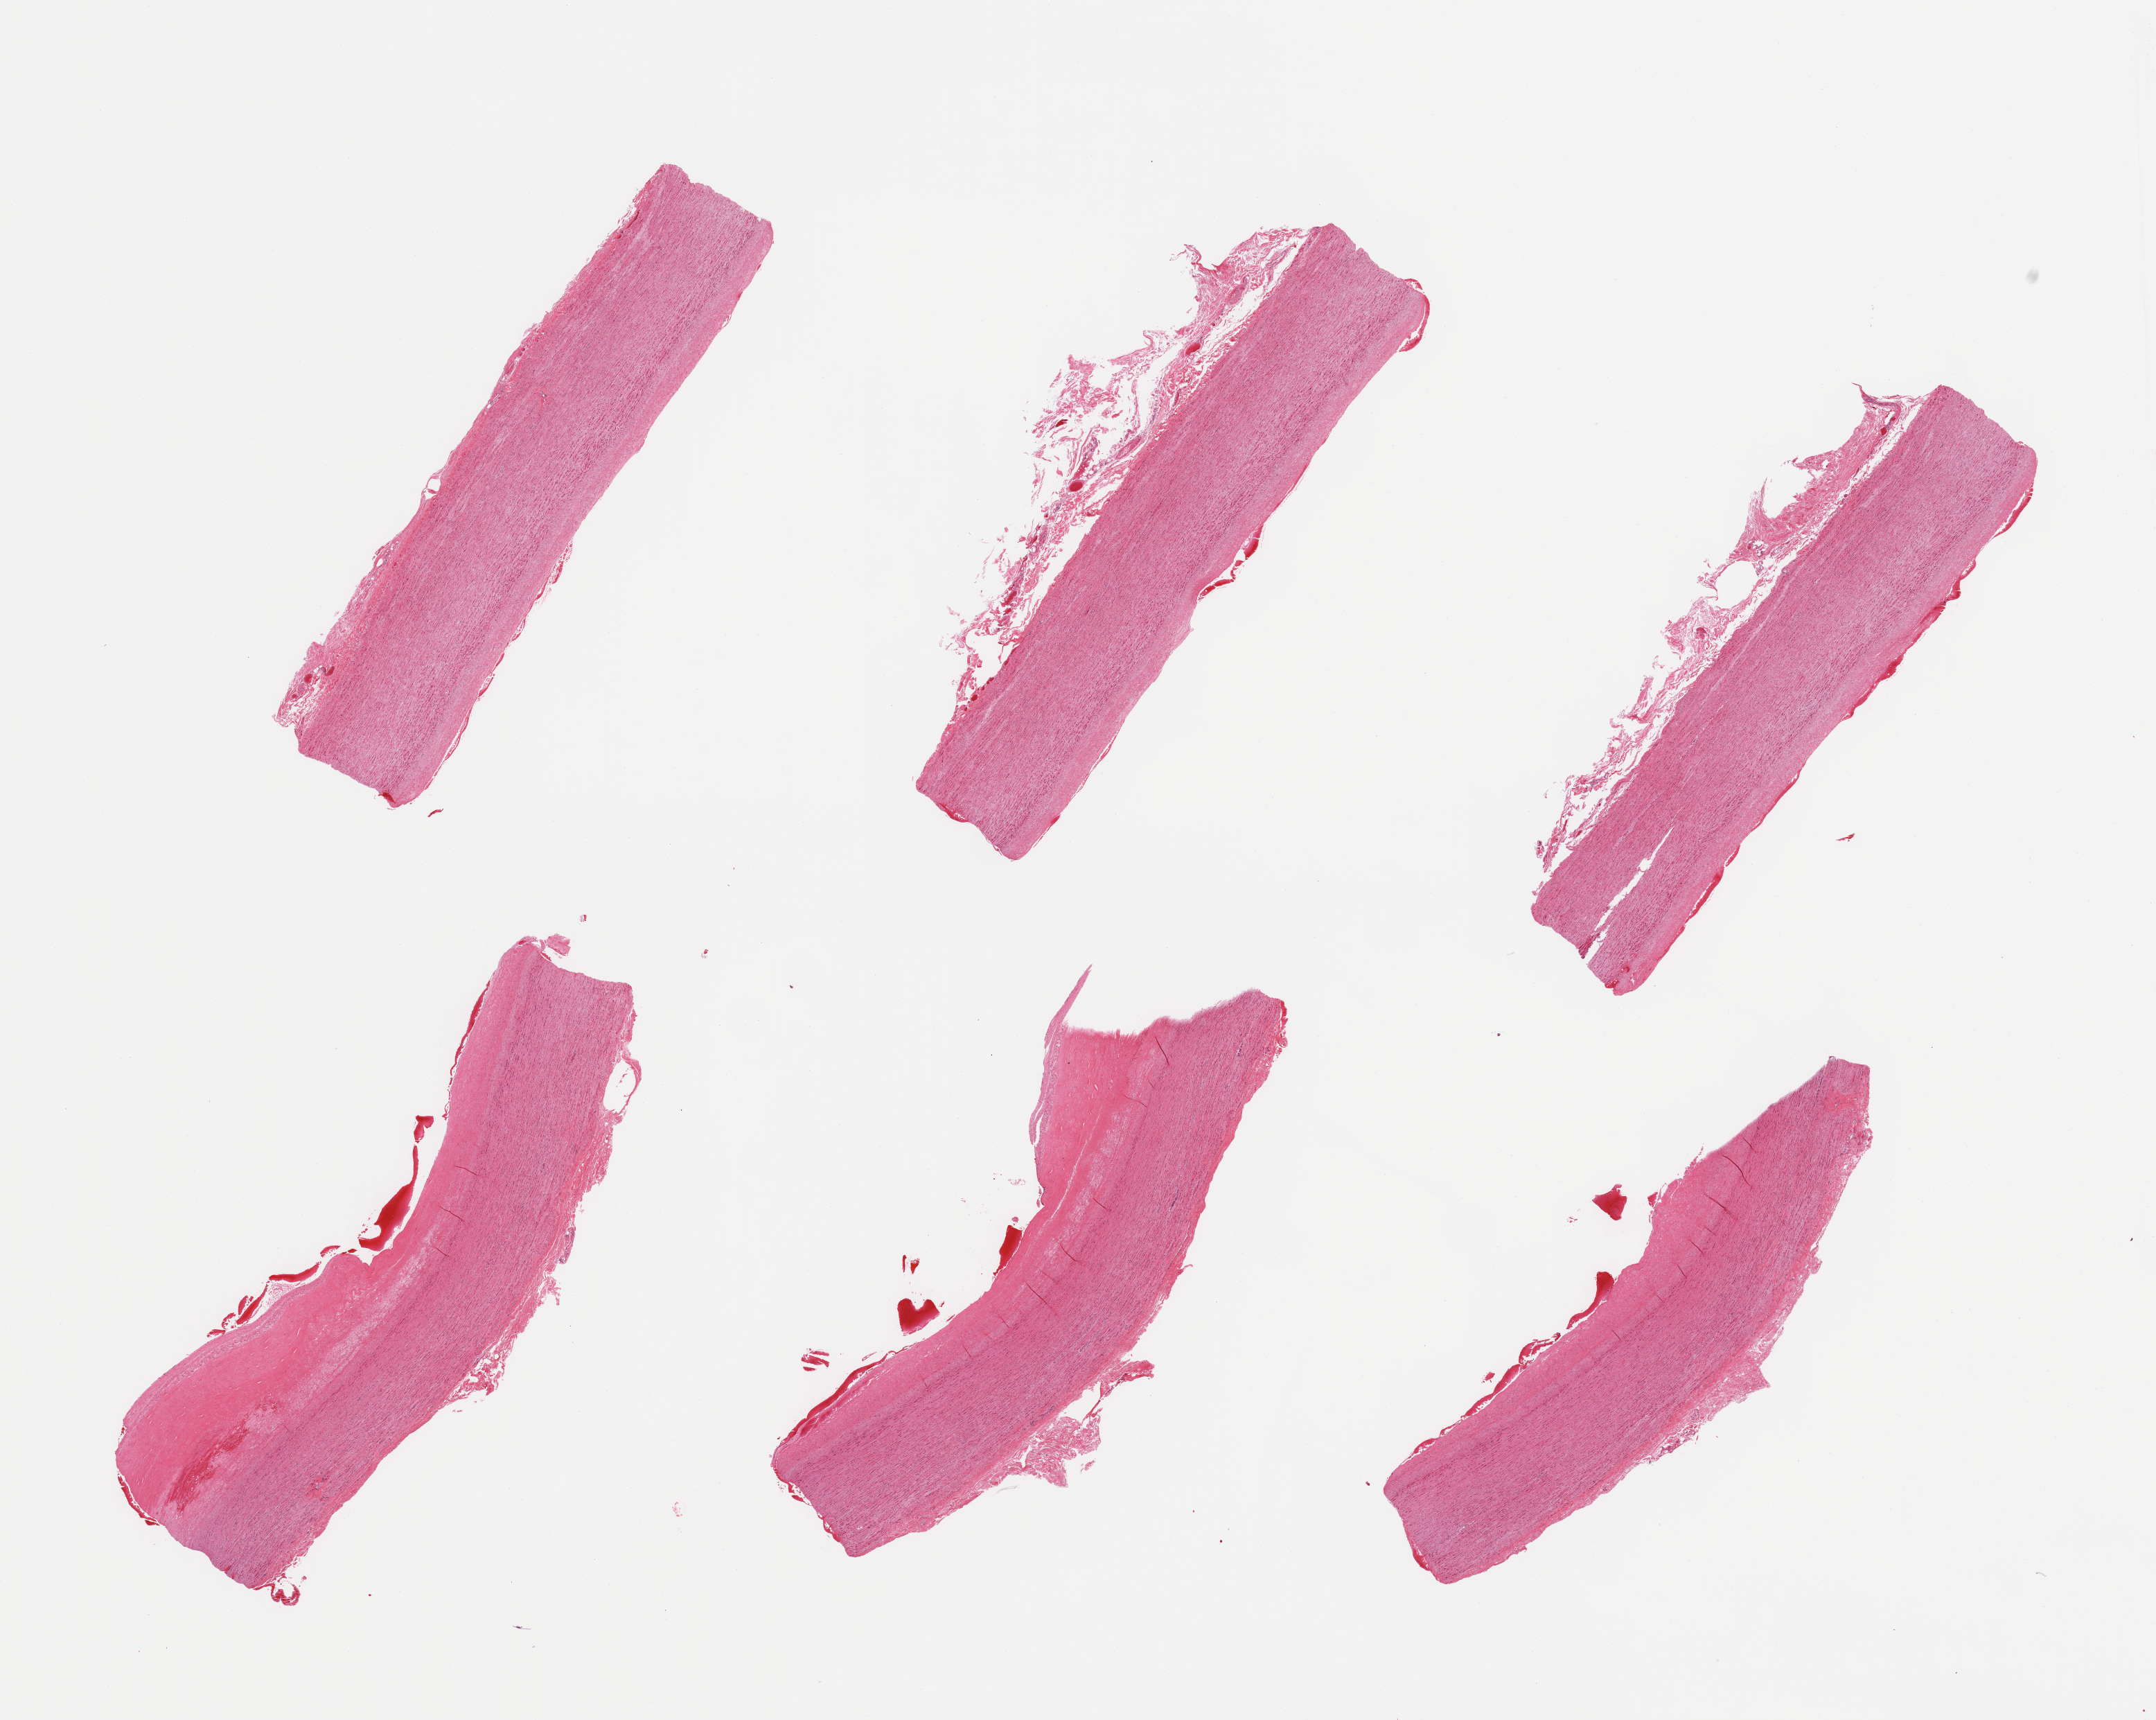
Whole-slide image, H&E stain — a low-resolution overview of the entire scanned area, about 24.6 x 19.6 mm (acquisition: 20x scan), PAXgene-fixed paraffin-embedded (PFPE) section, target tissue: aorta, donor tissue sample. Donor sex: male.
Review note (as recorded): 6 pieces; flat fibrous and fatty plaques up too 1mm thick.